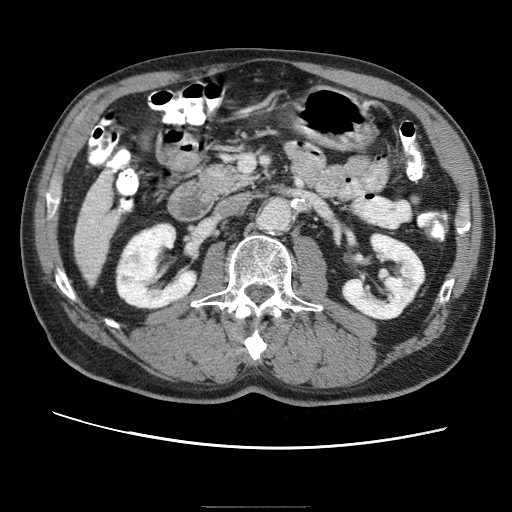
Contrast-enhanced abdominal CT (liver protocol), one axial slice. Position 8 of 75 along the scan axis. Reconstruction kernel STANDARD. One of 2 acquisitions stored at this slice position. Soft-tissue window (W 400 / L 40 HU). 2.5 mm slice thickness. 512 × 512 image matrix, field of view 360 × 360 mm. Case-level facts recorded for this patient, not image findings: diagnosis: hepatocellular carcinoma (patient treated with transarterial chemoembolisation; whether this scan precedes or follows treatment is not stated here); TNM stage (as recorded): Stage-II; Child-Pugh class: A; tumour differentiation: well differentiated; tumour nodularity: multinodular.
Structures marked on this image (semi-automatic segmentation, software-assisted and operator-edited):
- liver parenchyma outside the tumour (the mass and vessels are separate outlines, so this box may not span the whole liver): bounding box [x1, y1, x2, y2] px = [76, 178, 104, 270]
- liver vessels: [81, 180, 102, 249]